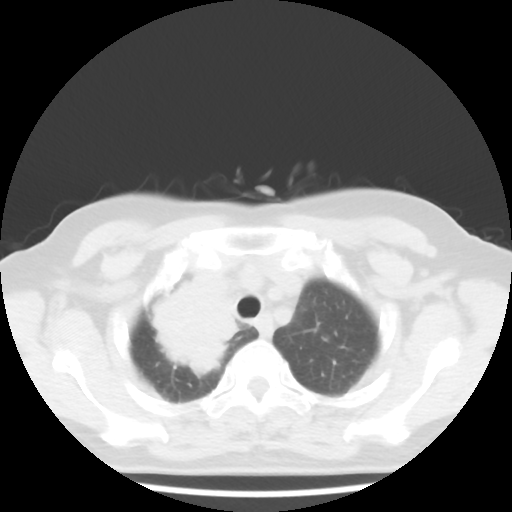
Chest CT, one axial slice. Slice 36 of 43 in the series (ordered by position). Lung window (W 1500 / L -600 HU). 5 mm slice thickness. 512 × 512 image matrix, field of view 316 × 316 mm. Female patient, age 62 years. Case-level facts recorded for this patient, not image findings: clinical TNM (as recorded): T3 N0 M0; histopathological grade: G3.
Annotated regions visible in this slice (rectangle marked by the reading radiologist):
- lung tumour (recorded histology: small cell carcinoma): bounding box (x1, y1, x2, y2) in pixels: (144, 264, 251, 383)